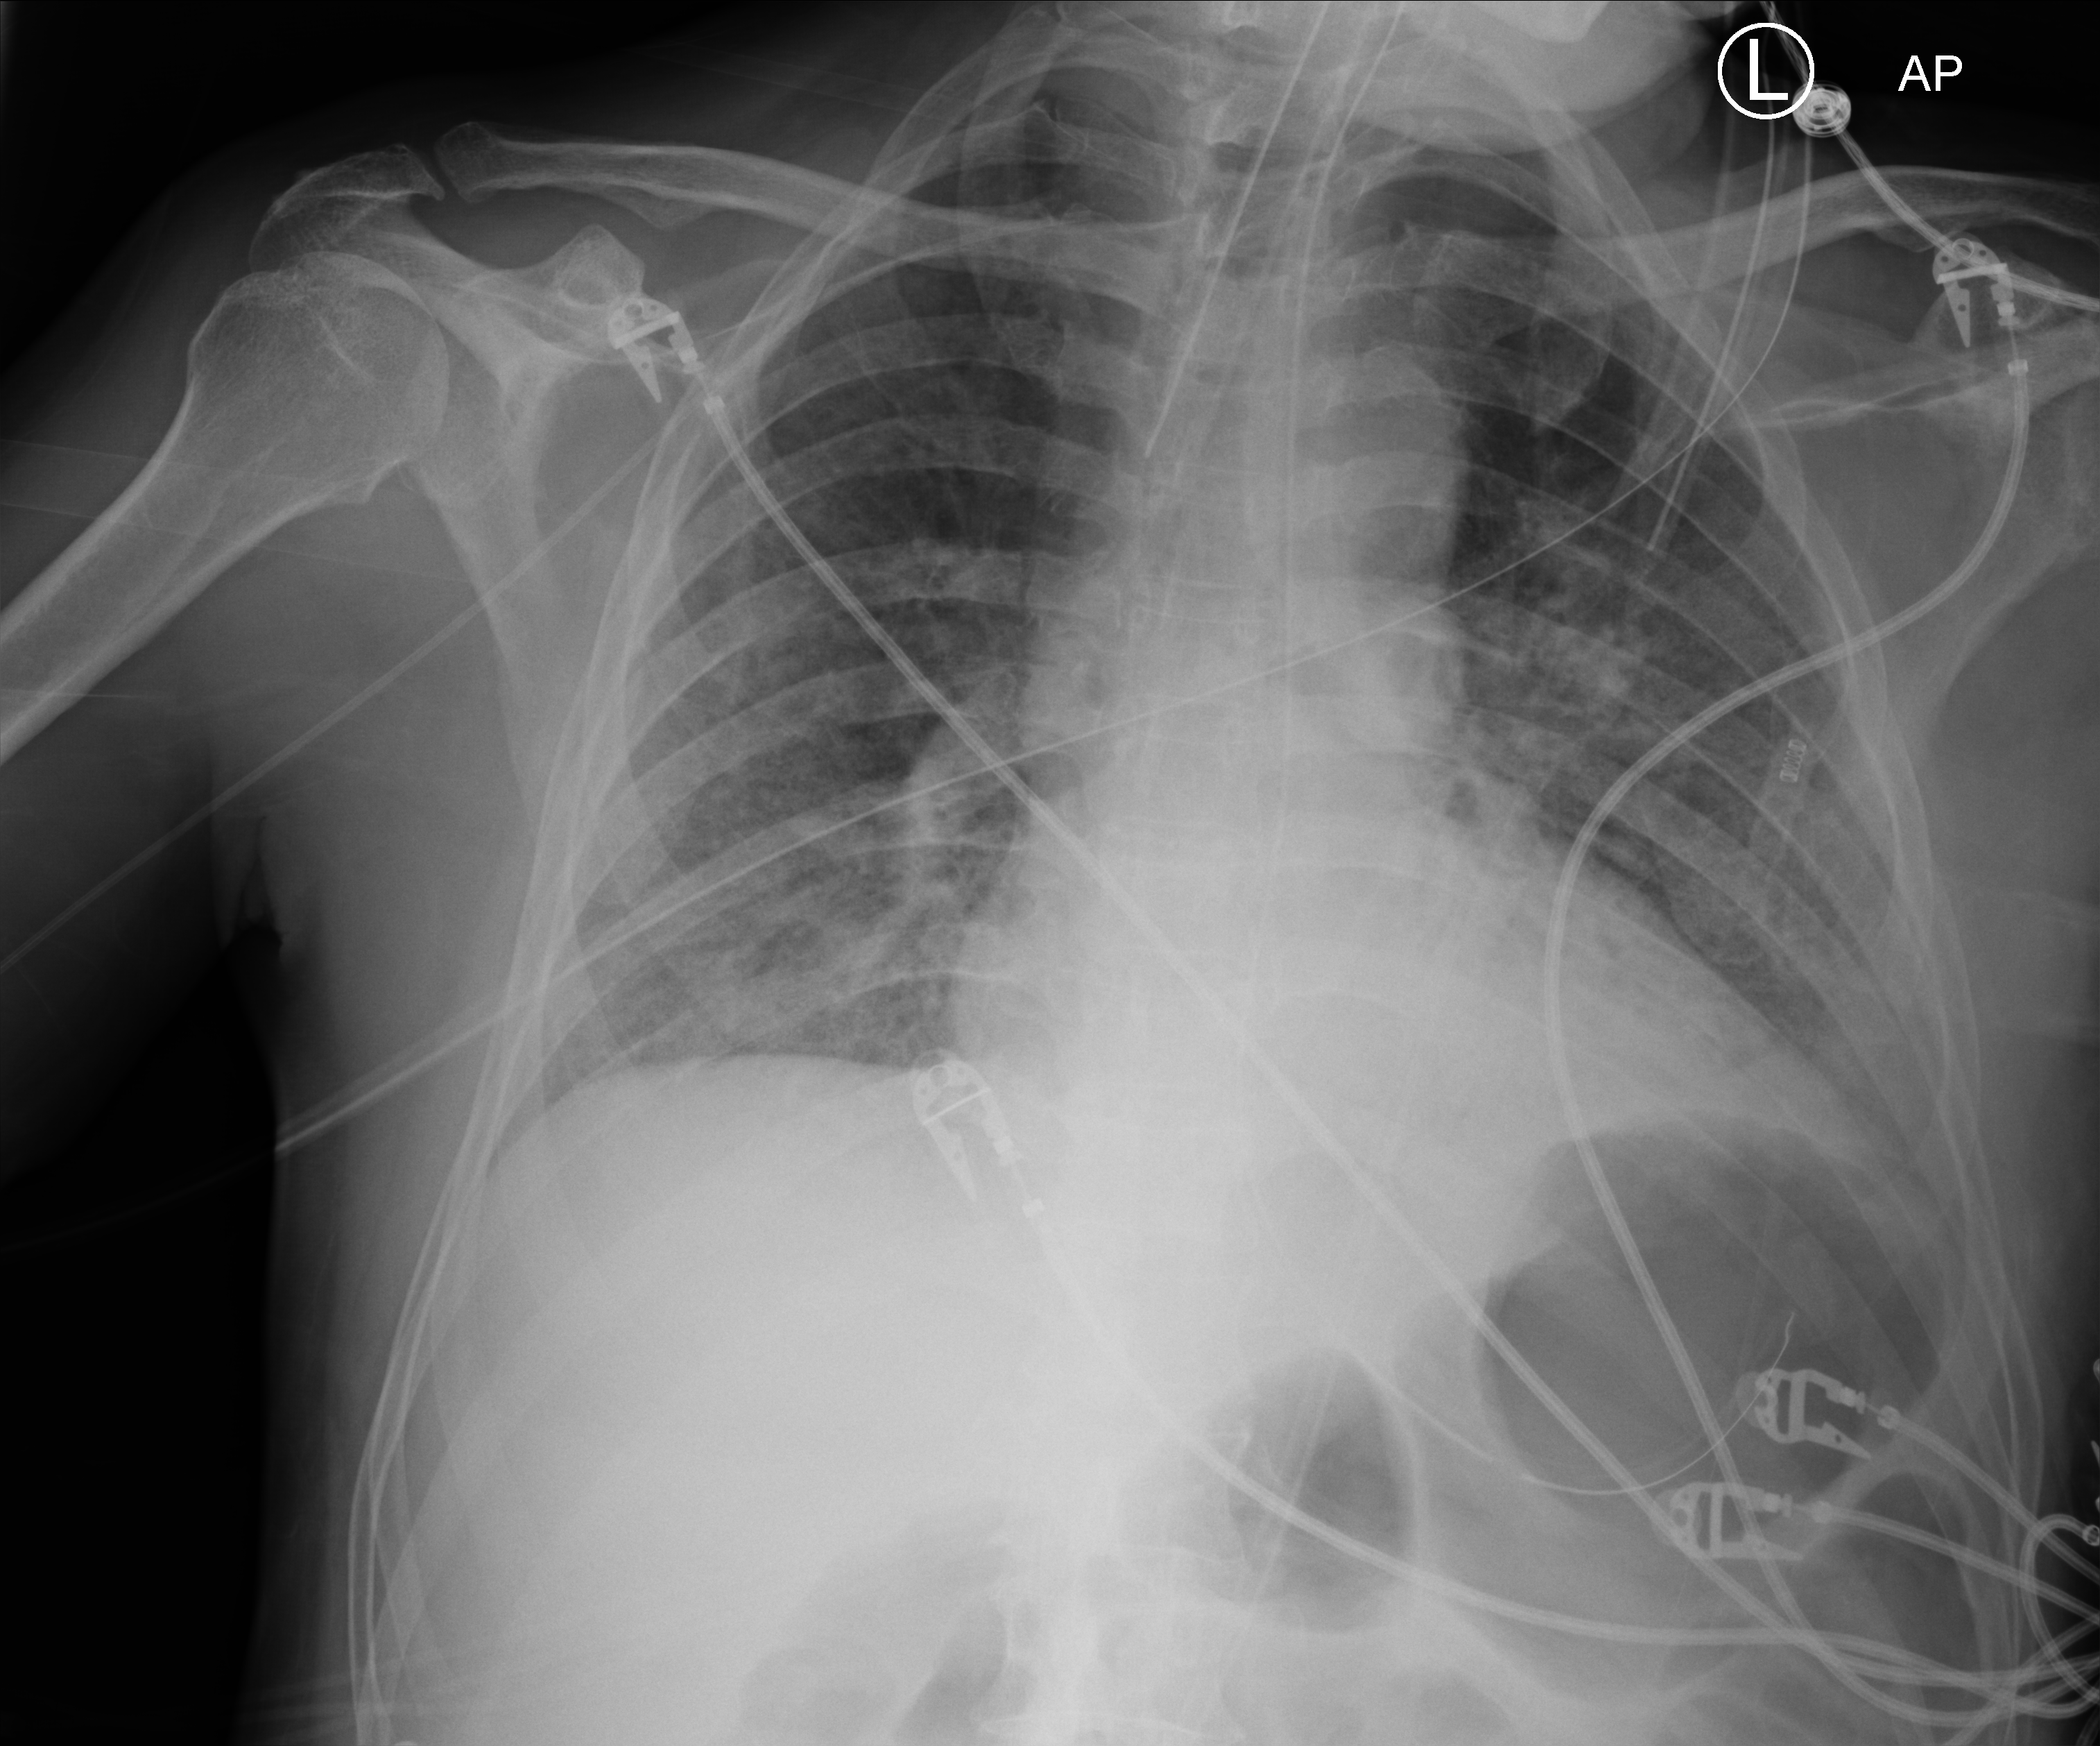
Bedside chest radiograph (computed radiography). Patient hospitalised with COVID-19; male, aged 60–74 years.
Hospital-stay facts (about this admission, not read from this image; timing relative to this image not recorded): length of hospital stay: 37 days; mechanically ventilated during this hospital stay: yes; admitted to intensive care during this hospital stay: yes.